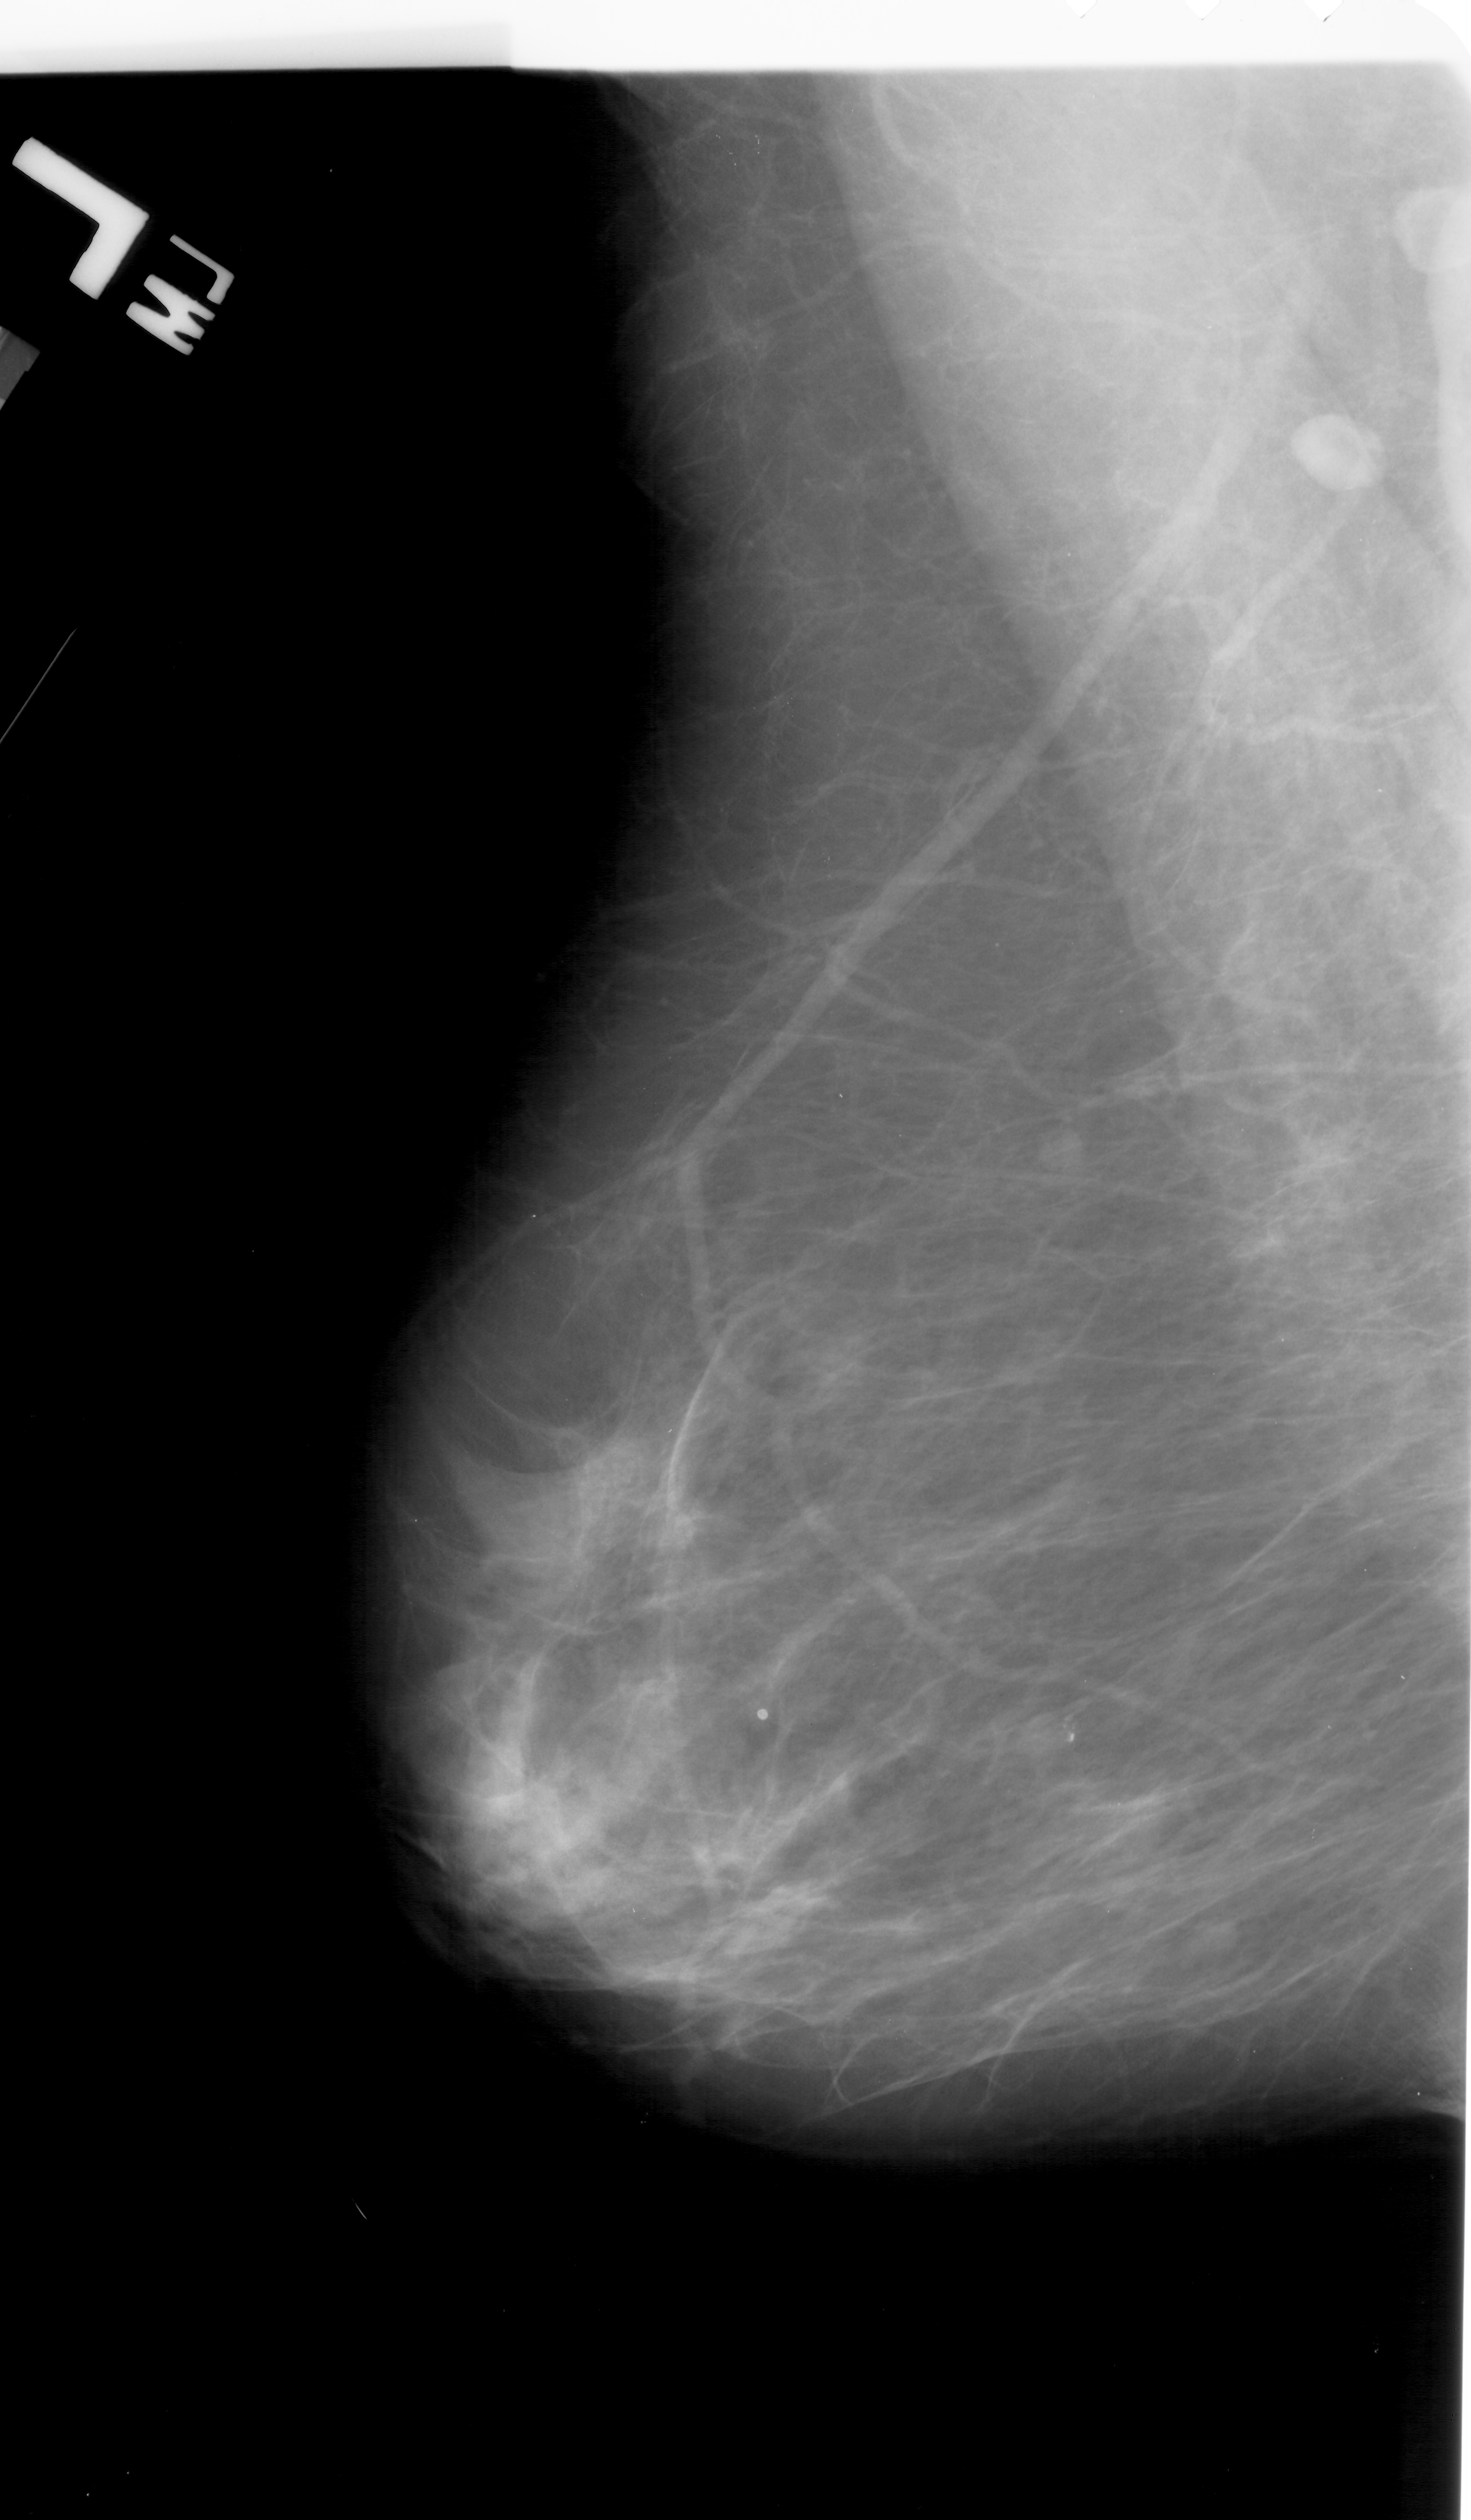
Digitized screen-film mammogram; left breast; mediolateral oblique (MLO) view; BI-RADS breast density category 2 (scale 1–4); 1471 × 2520 image matrix.
Expert-marked regions of interest on this film, with their recorded descriptors:
- calcifications, morphology pleomorphic, distribution linear; BI-RADS assessment category 4; pathology result (as recorded, not read from the image): malignant: bounding box [x1, y1, x2, y2] px = [1038, 1713, 1074, 1766]